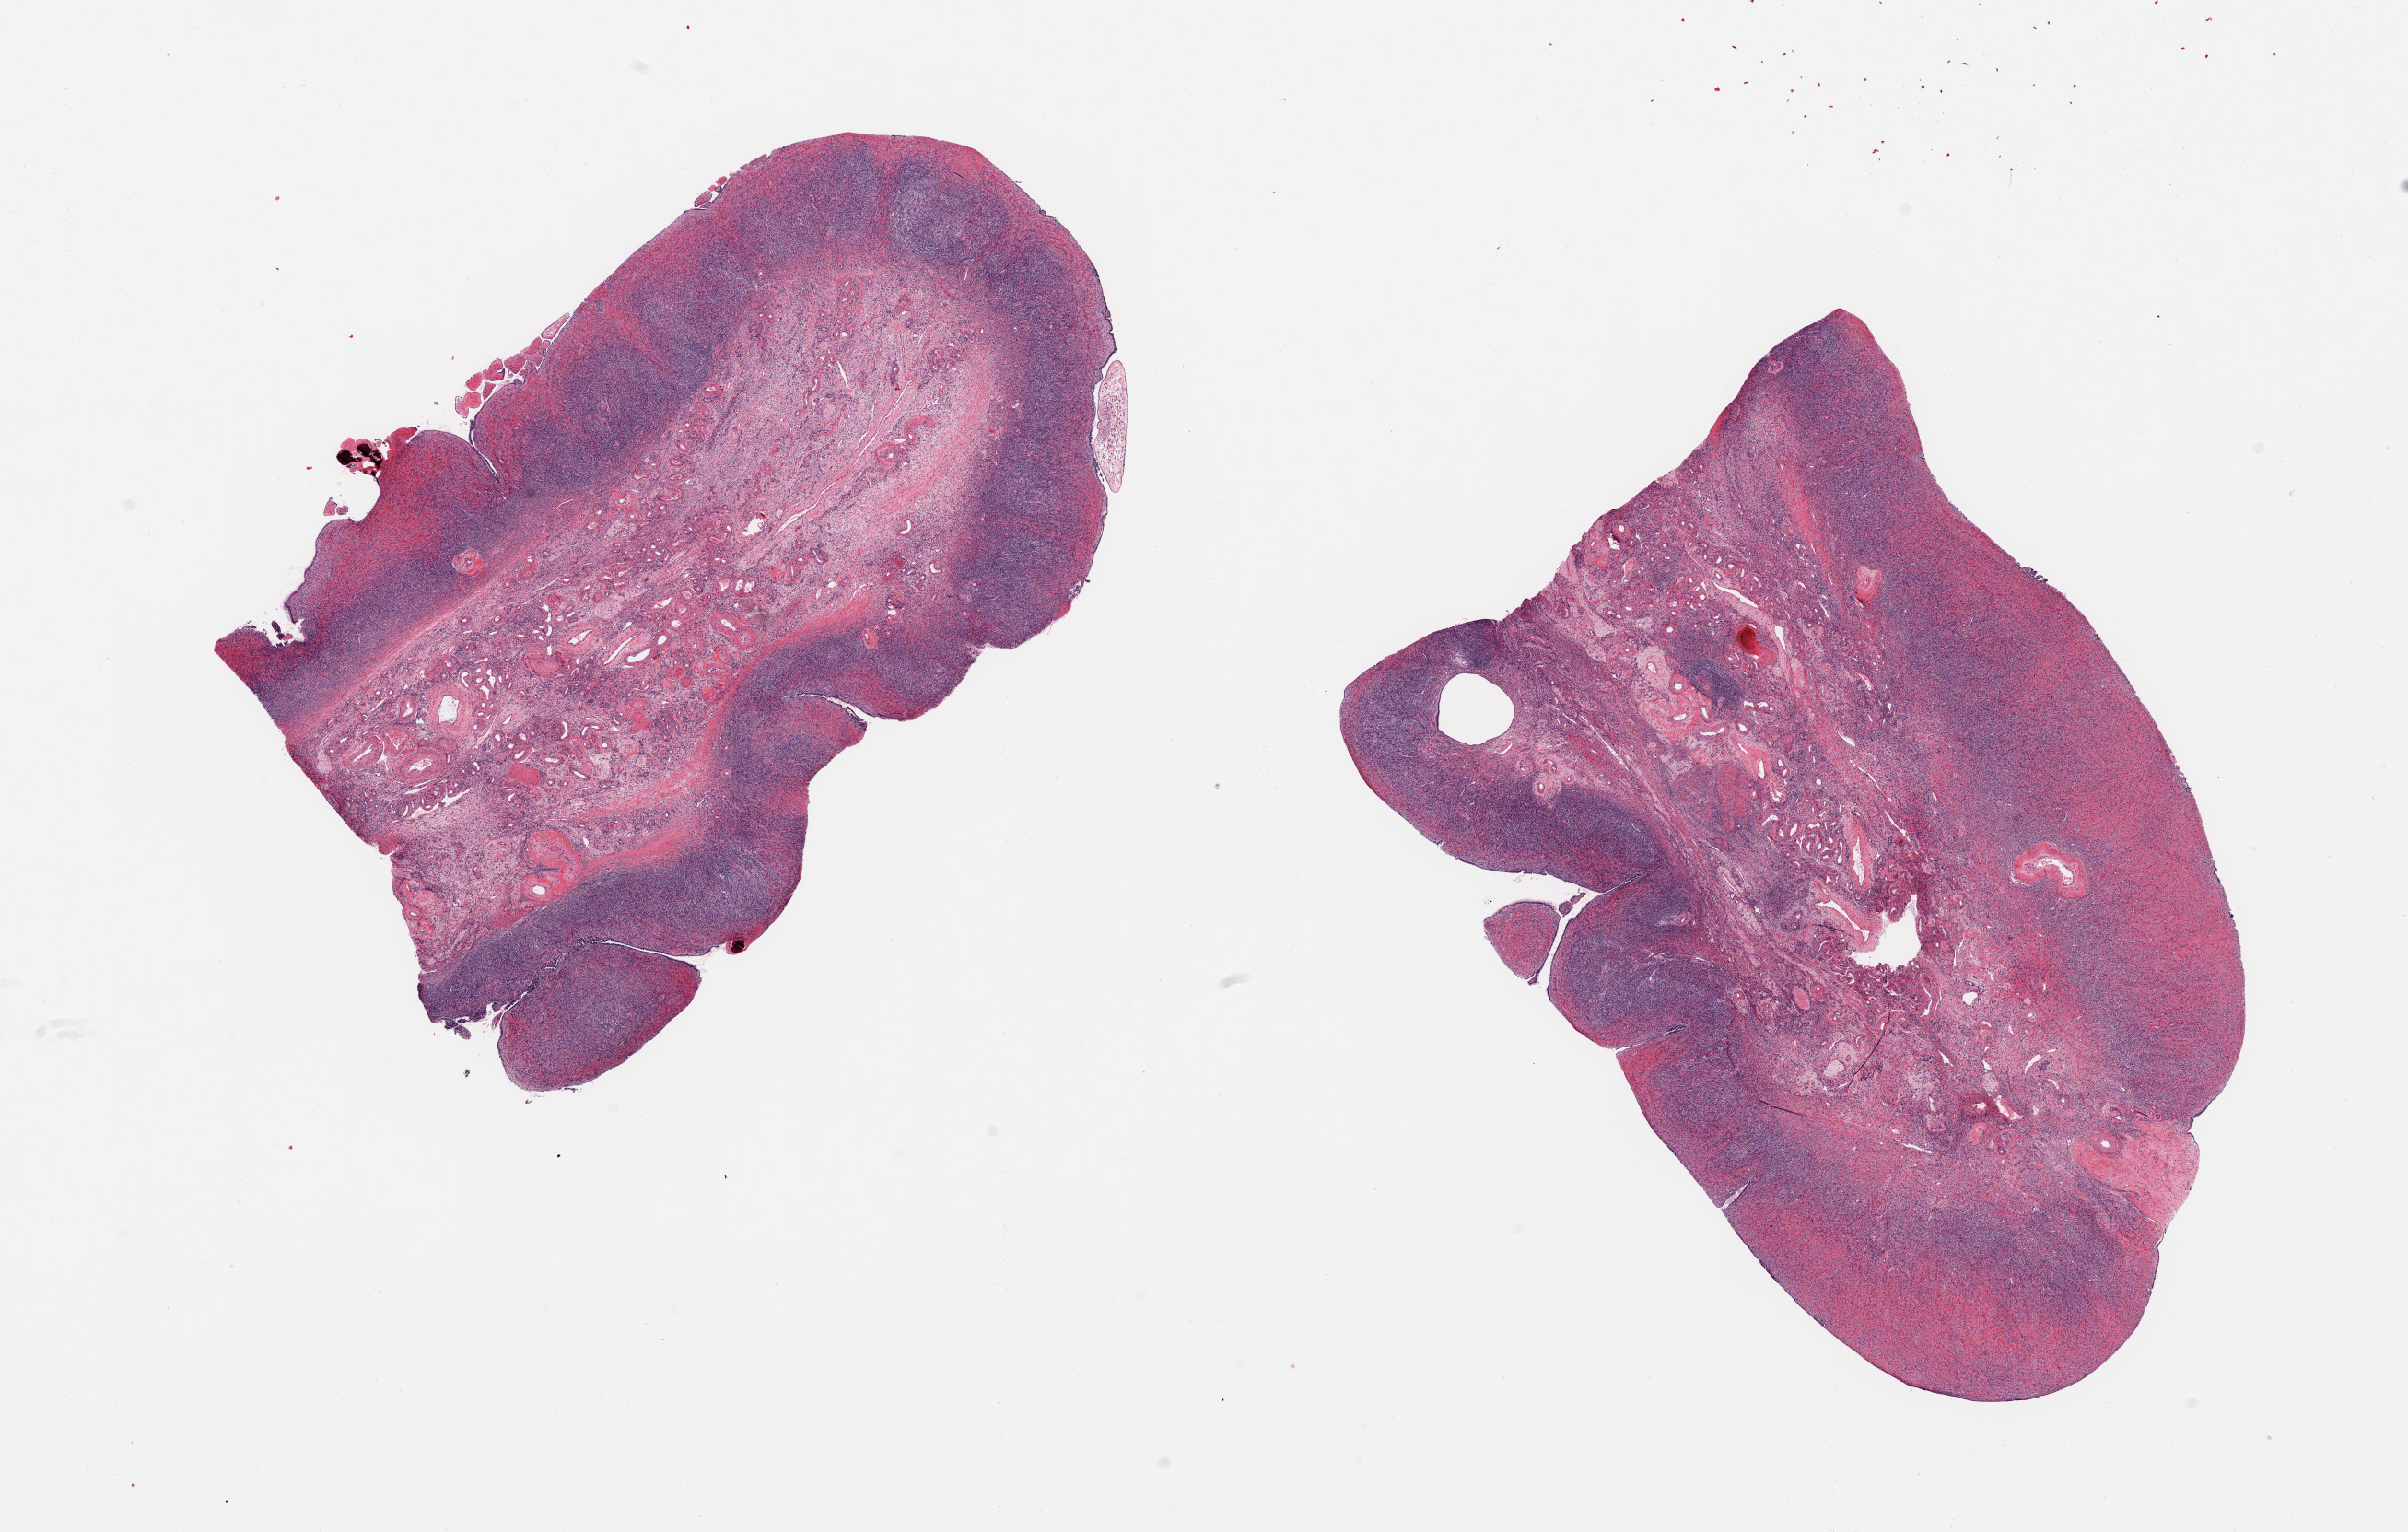
Whole-slide image, haematoxylin and eosin stain, brightfield, a low-resolution overview of the entire scanned area, about 20.7 x 13.2 mm (acquisition: 20x scan). PAXgene-fixed, paraffin-embedded tissue. Section of ovary (target tissue). Donor tissue sample.
Pathologist's review note for this sample: 2 pieces; atrophic.